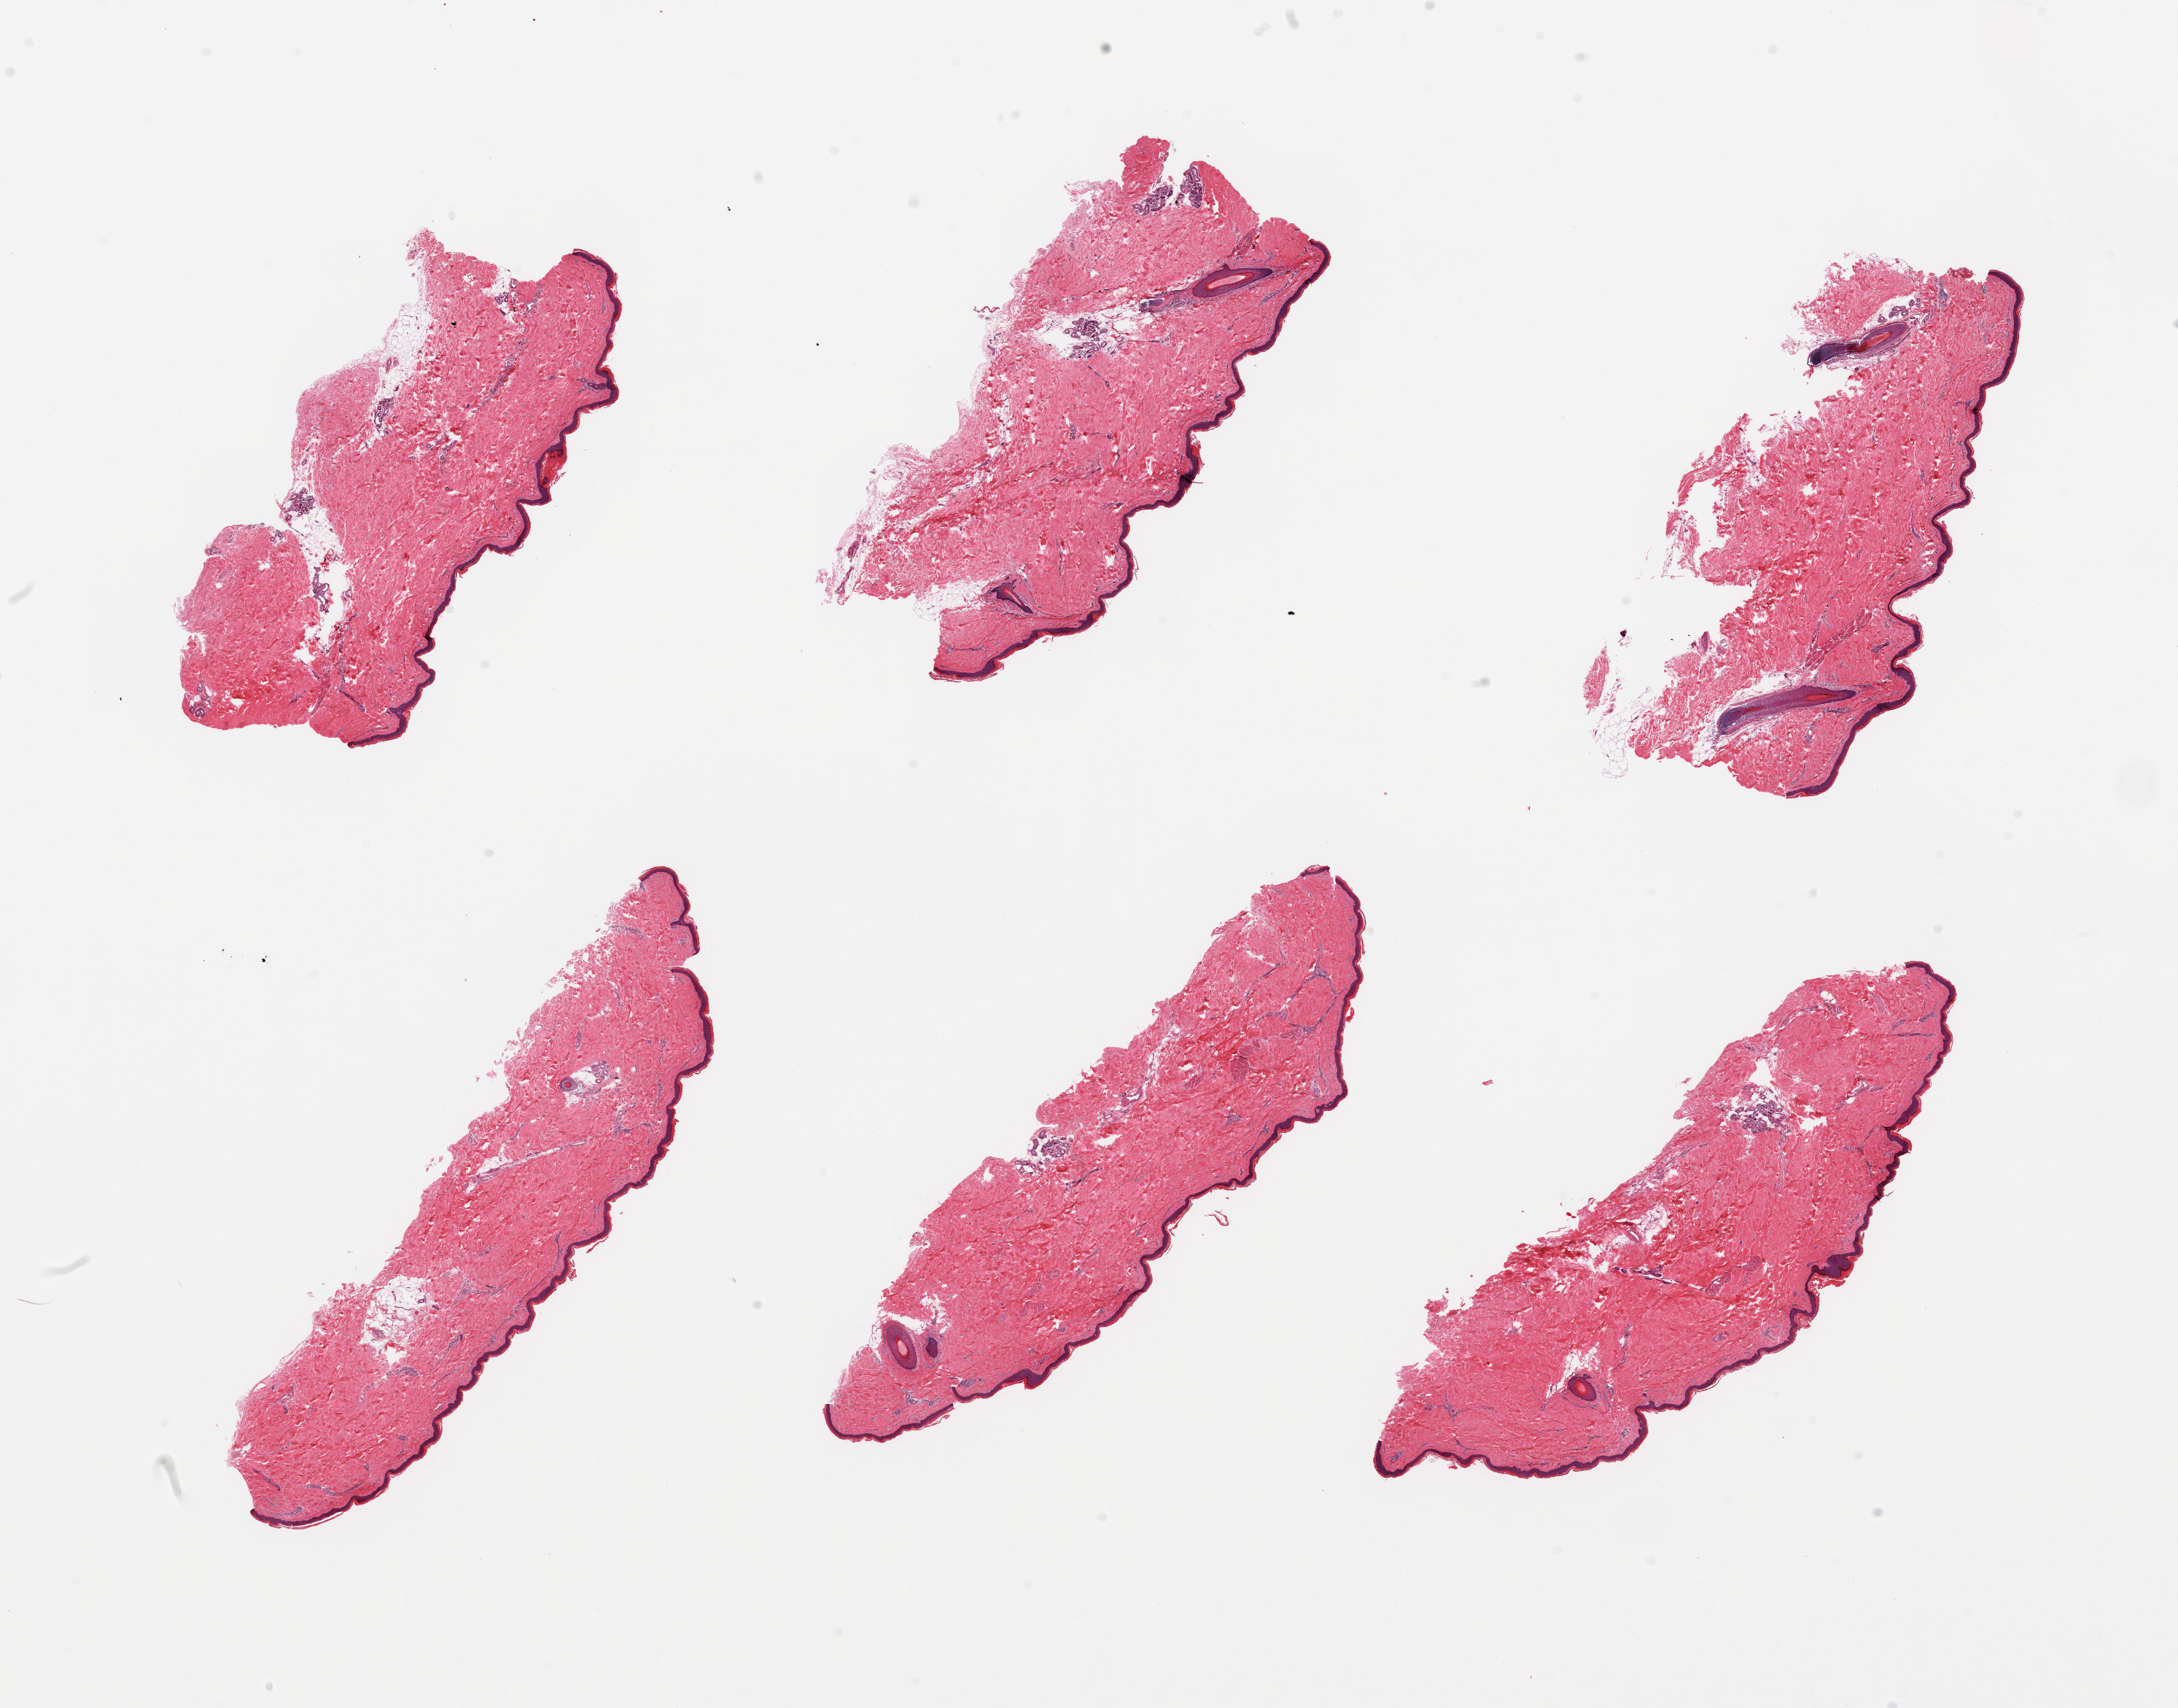
Haematoxylin and eosin whole-slide image, a low-resolution overview of the entire scanned area, about 23.6 x 18.5 mm (acquisition: 20x scan). PAXgene-fixed paraffin-embedded (PFPE) section. Sampled site (target tissue): skin of lower leg. Tissue donor sample. Donor: male.
Reviewer comment on this tissue sample: 6 pieces; epidermis measures about 44 microns, small portion of internal (periadnexal) fat.